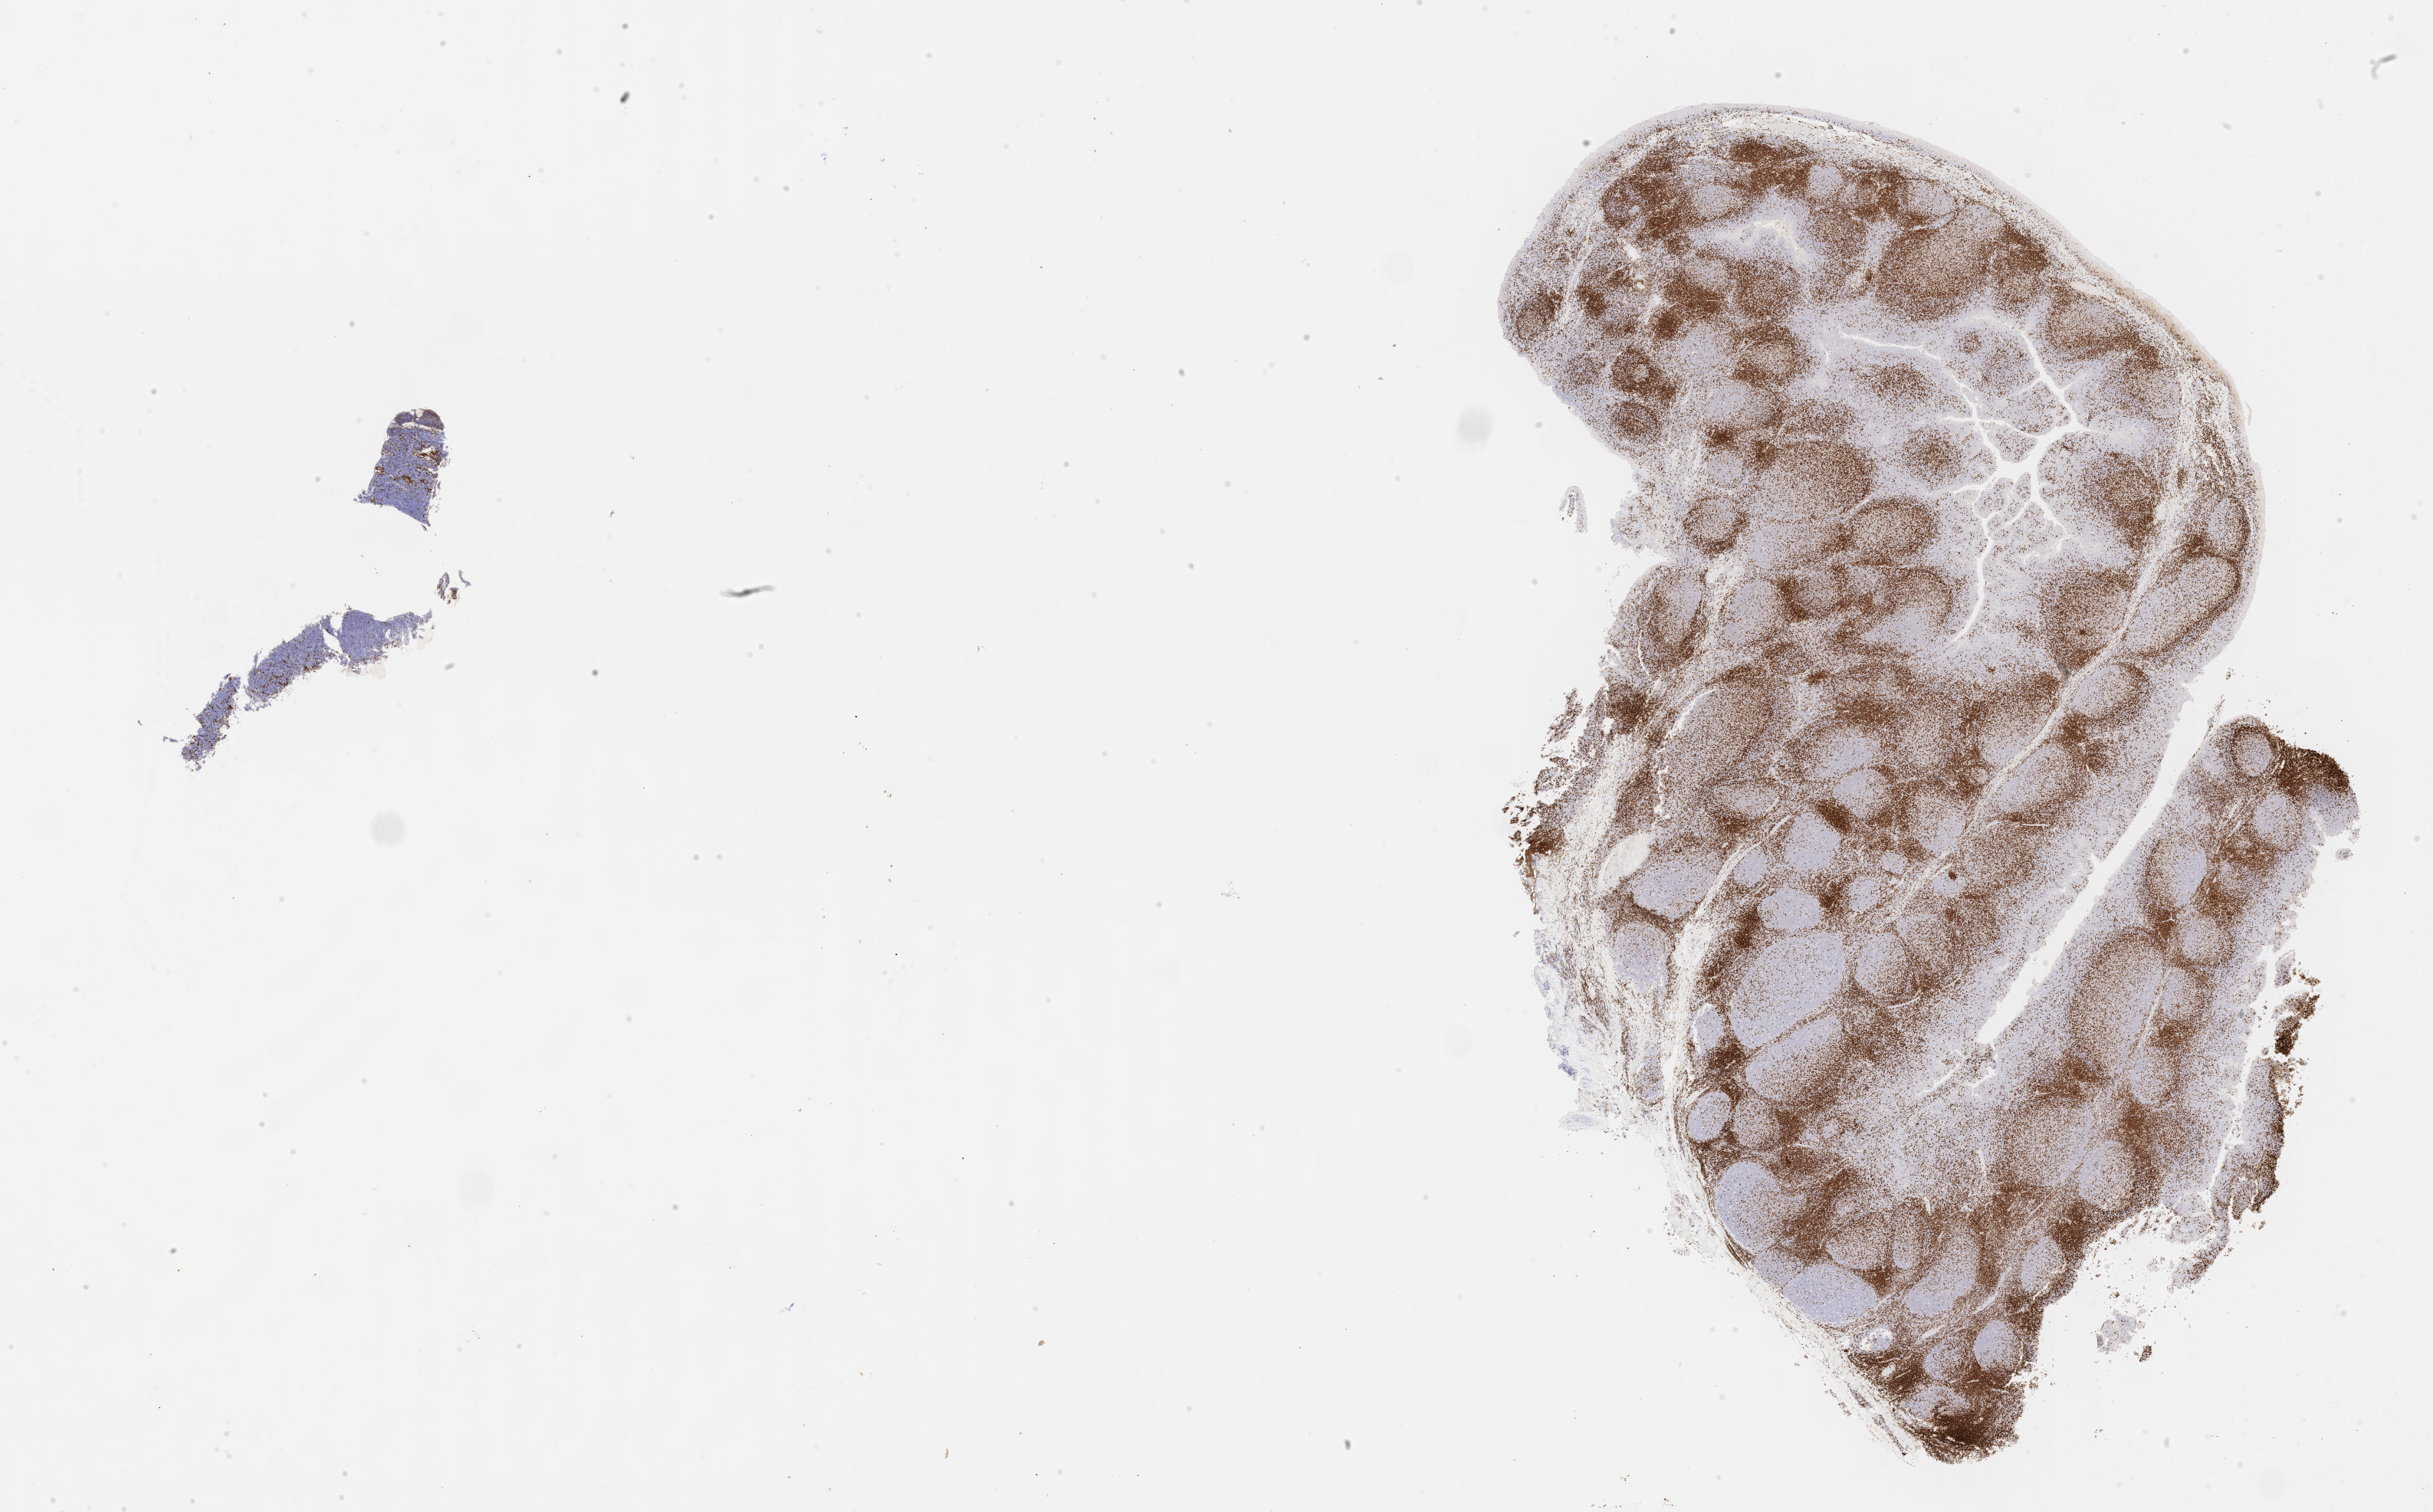
IHC for CD3, whole-slide image, shown as a low-resolution overview of the whole scanned area (about 25.7 x 16.0 mm). Specimen: tumor tissue. Anatomic site: cranium. Male patient; age at initial diagnosis 6 years.
Histologic diagnosis: Burkitt lymphoma, NOS.